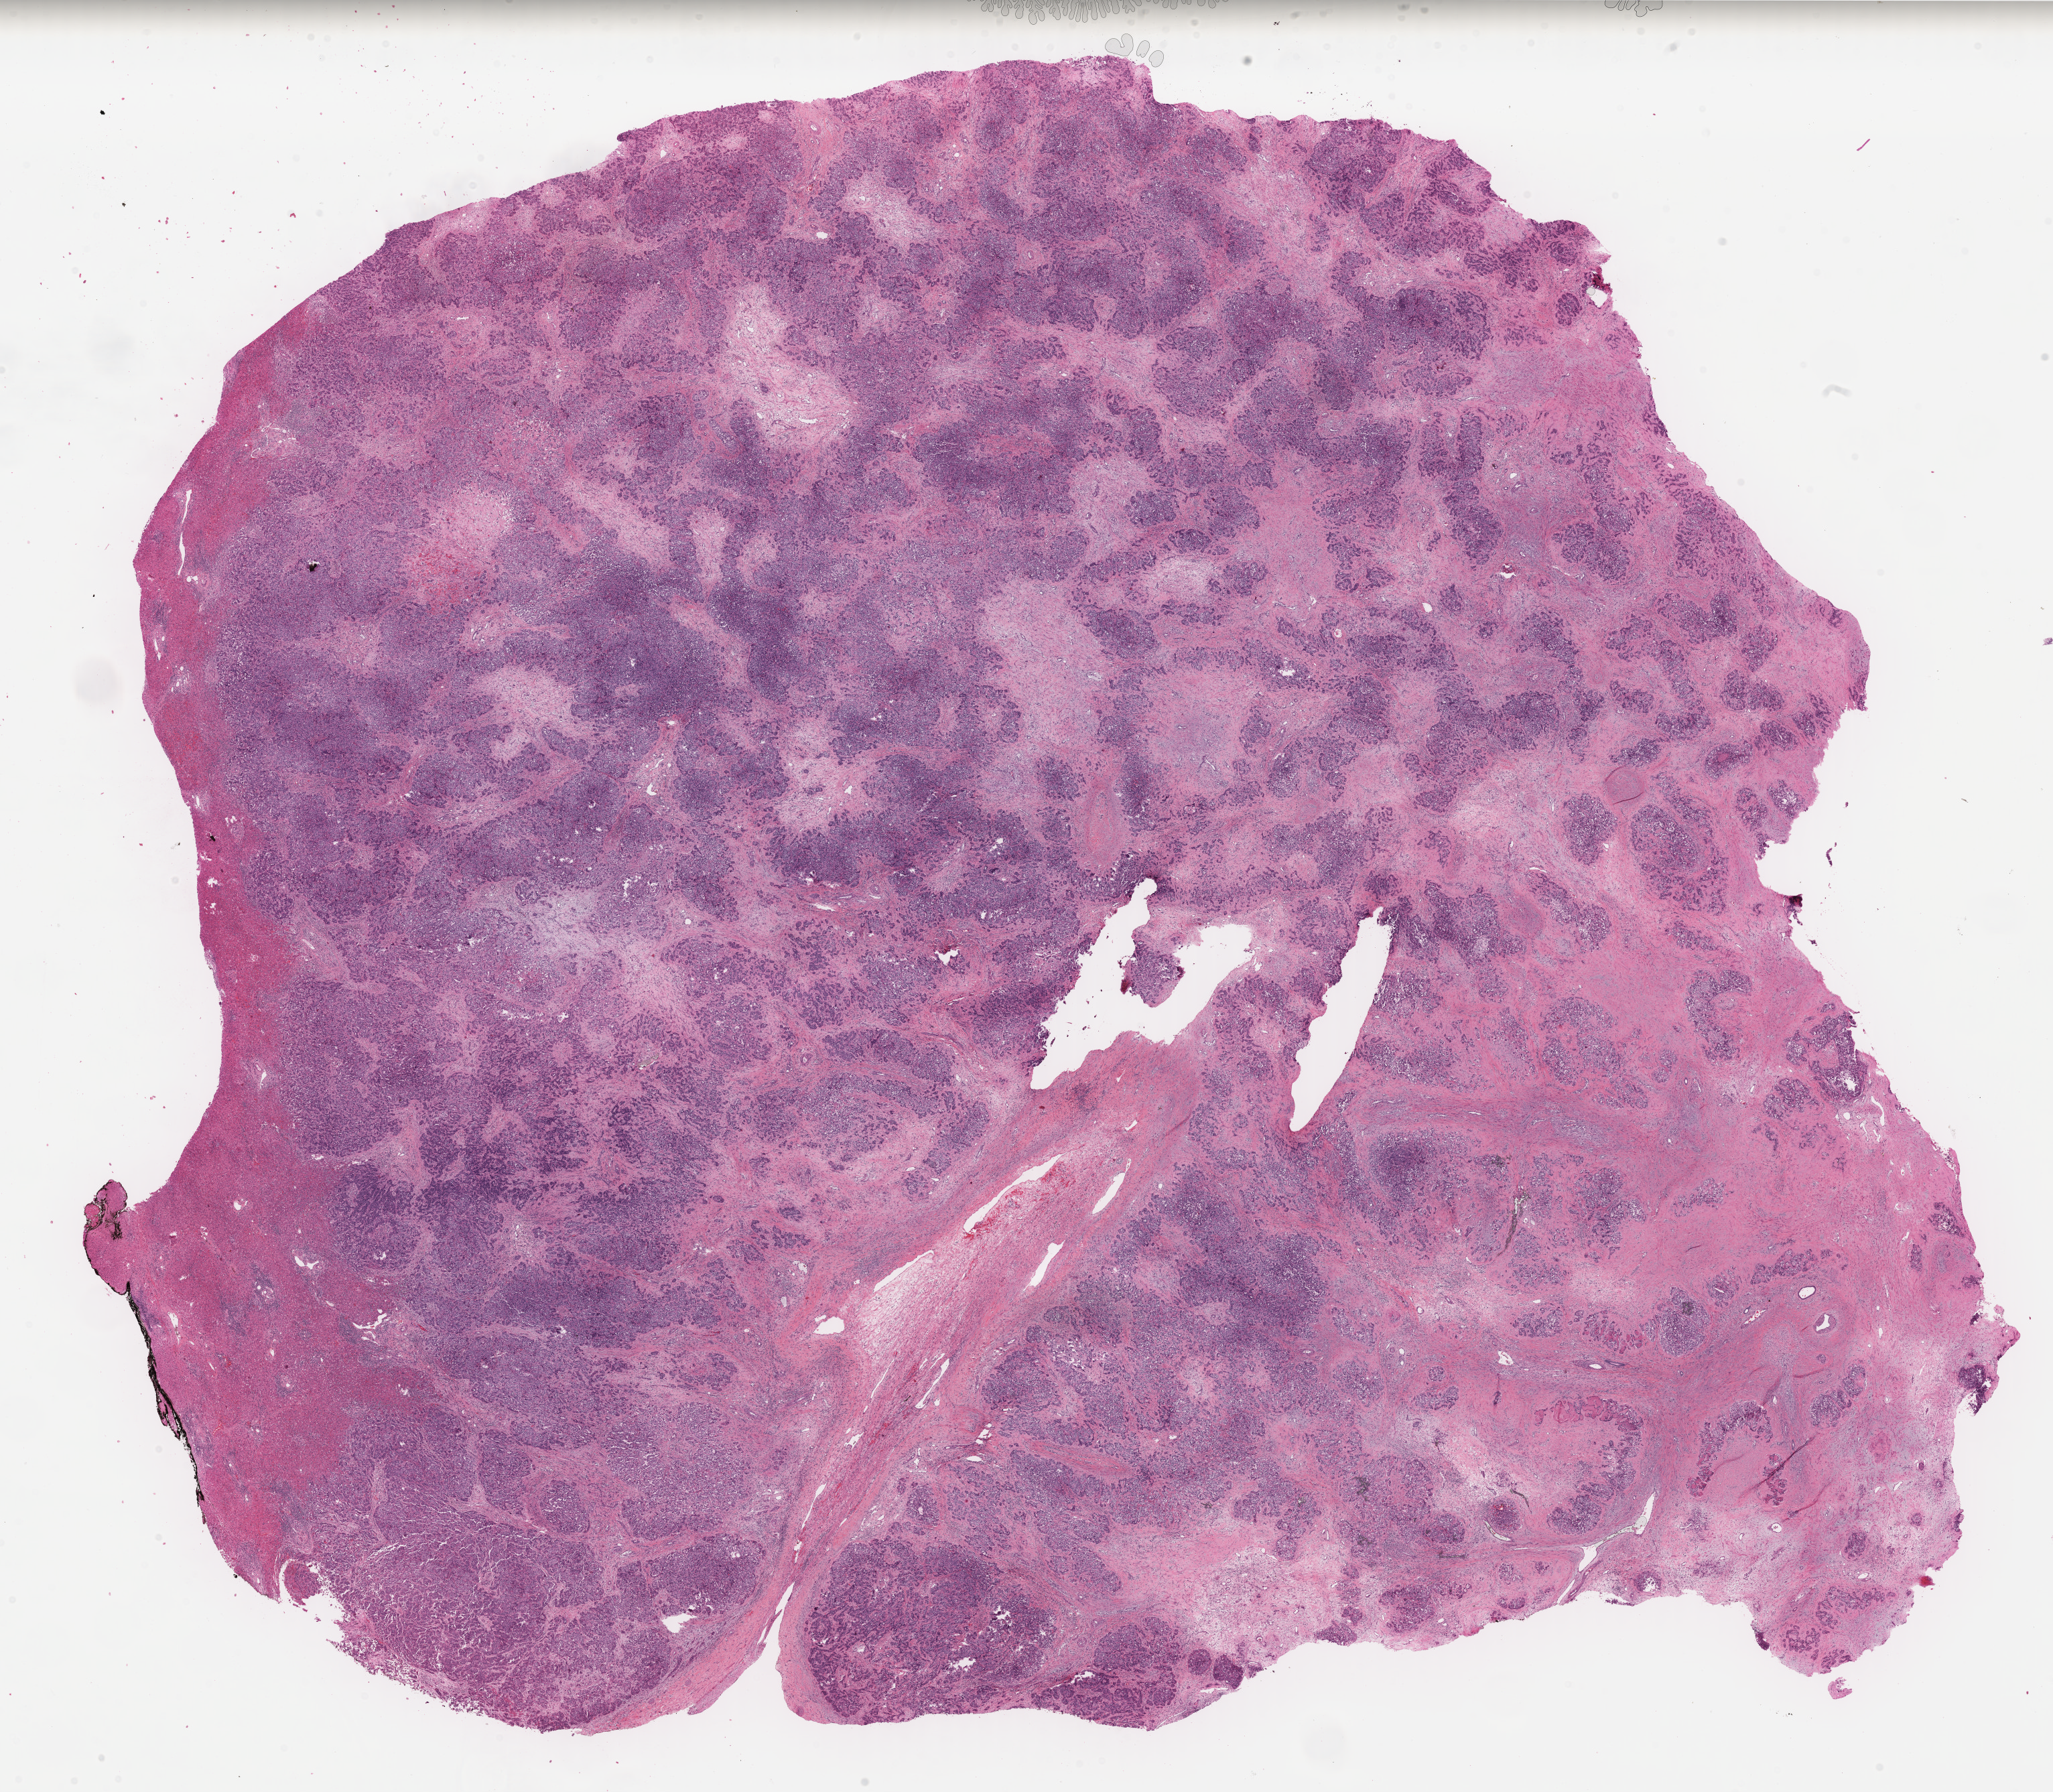
H&E-stained whole-slide image, a low-resolution overview of the entire scanned area, about 24.2 x 21.2 mm (slide scanned at 40x); formalin-fixed paraffin-embedded (FFPE) diagnostic section; primary tumour sample from the bile duct. Male, age 58 years at initial diagnosis. Histologic grade: G3 (poorly differentiated).
TNM: T1 N0 M0. Diagnosis: Cholangiocarcinoma (intrahepatic bile duct). AJCC pathologic stage: I (7th edition).